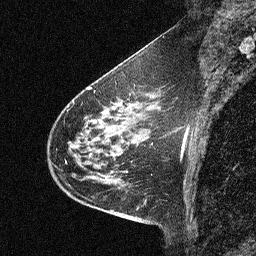
Breast MRI (dynamic contrast-enhanced), one sagittal slice. Dynamic contrast-enhanced study with each time point stored as its own series, time point 2 of 3 at this slice position (early post-contrast, ordered by acquisition time). 1.5 T. TE 4.5 ms, TR 11 ms. 2.06 mm slice thickness. 256 × 256 image matrix. Patient: female, 46 years. Case-level facts recorded for this patient, not image findings: setting: breast cancer imaged before/during neoadjuvant chemotherapy; receptor status: HER2-positive.
Annotated regions visible in this slice (semi-automatically segmented with operator editing):
- analysis volume of interest (the breast-tissue region the enhancement analysis was run in; not a lesion): bounding box <42,80,150,180> (left, top, right, bottom; pixels)
- tumour enhancement mask (voxels above the 90 % enhancement threshold inside the analysis volume of interest): <69,104,135,160>